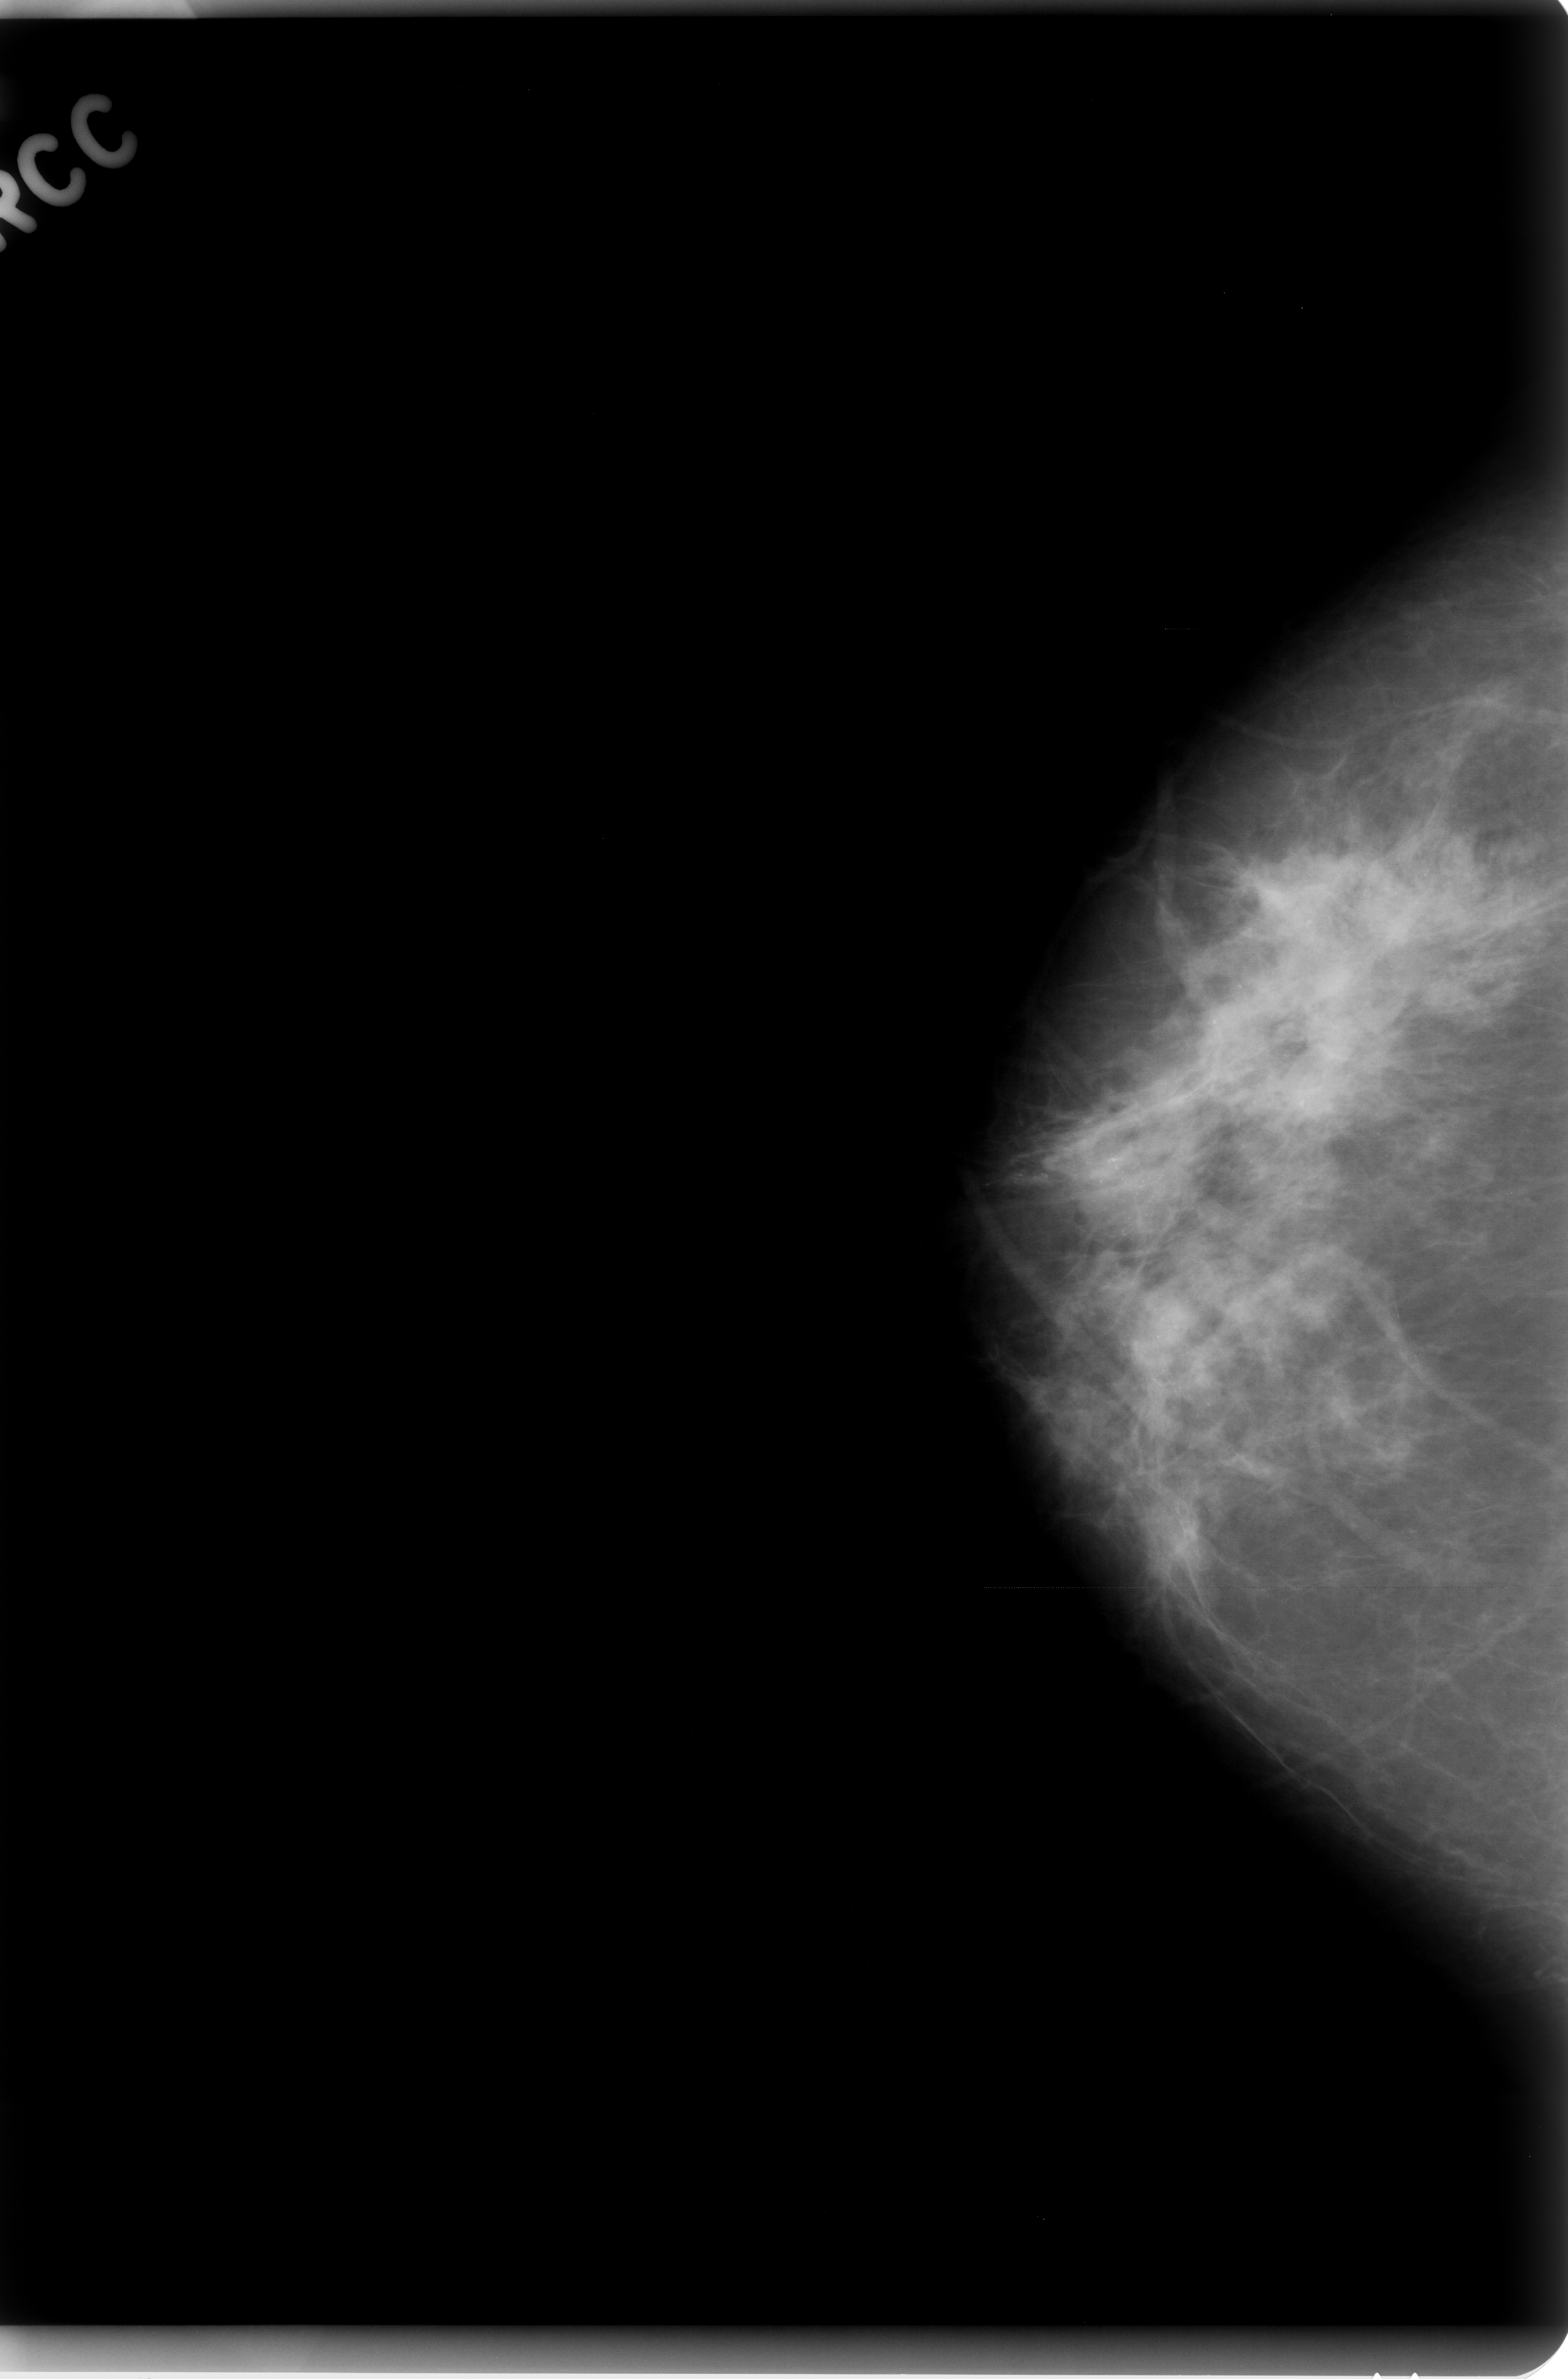
Mammogram (digitized film). Right breast. Craniocaudal (CC) view. Breast composition: scattered fibroglandular densities (BI-RADS density category 2 of 4). 1568 × 2379 image matrix.
Marked abnormalities (boxes around the expert regions of interest):
- calcifications, morphology pleomorphic, distribution regional; BI-RADS assessment category 5; subtlety rating 5 on a 1 (subtle) to 5 (obvious) scale; pathology (as recorded): malignant: box from (x=1005, y=683) to (x=1550, y=1582) px